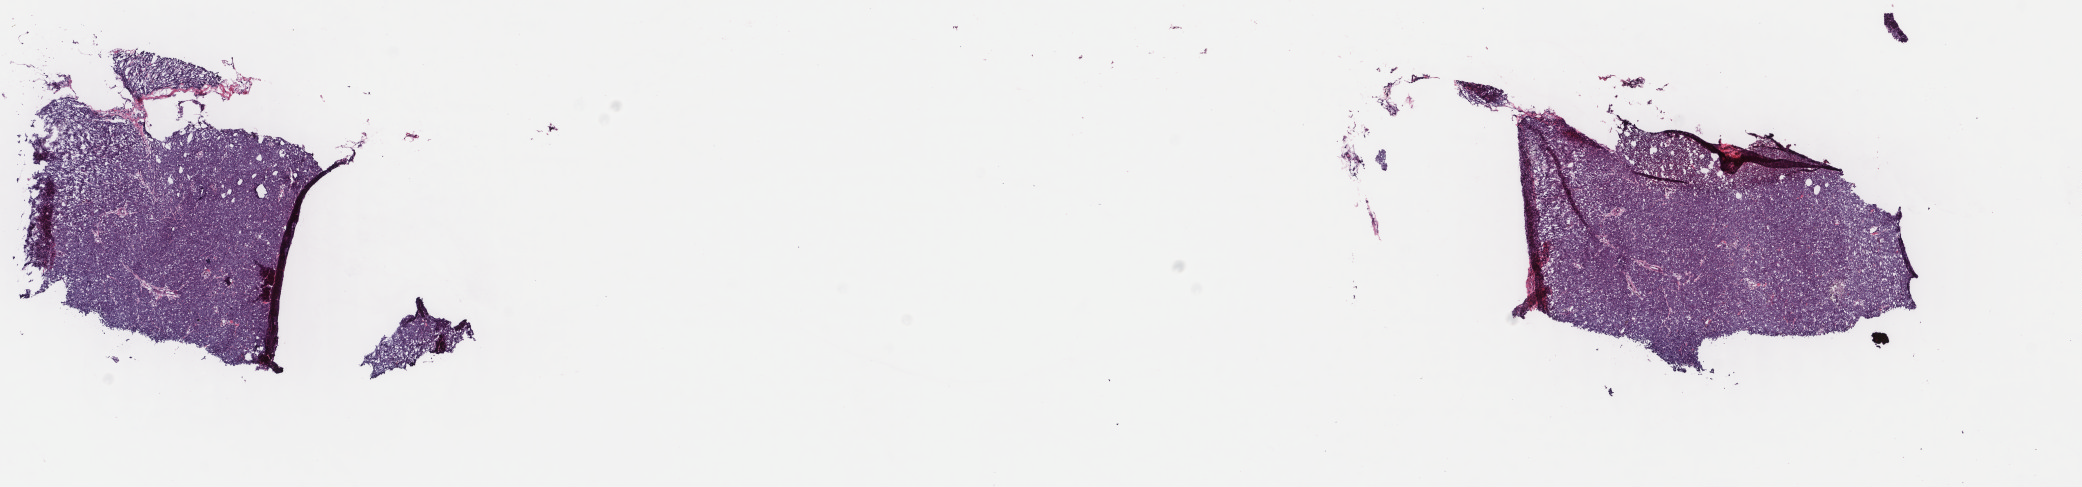
Digitized Hematoxylin and eosin (H&E) stained tissue section (whole slide), shown as a low-resolution overview of the whole scanned area (about 16.5 x 3.9 mm). Frozen section from the top of the tissue portion. Metastatic tumour sample, sampled site not recorded. Patient: male, age at initial diagnosis 69 years.
This section: metastatic tumour tissue. Patient diagnosis: Malignant melanoma, NOS.